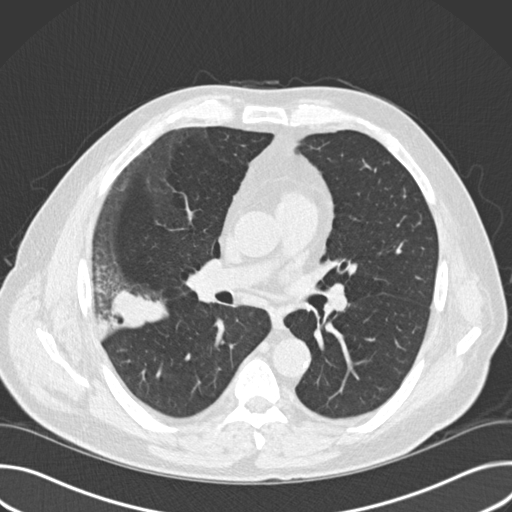
Low-dose screening chest CT, one axial slice; position 91 of 157 along the scan axis; reconstruction kernel B30f; lung window (W 1500 / L -600 HU); 2 mm slice thickness; 512 × 512 image matrix.
Outlined on this slice (outlined manually by an expert reader):
- lesion 1 (tumor, upper lobe of right lung): box from (x=111, y=290) to (x=168, y=328) px